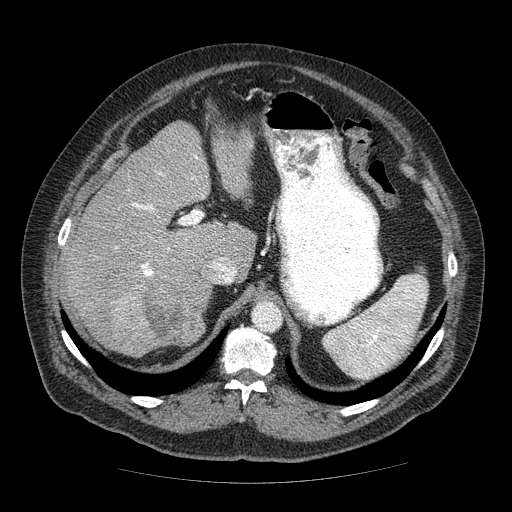
Contrast-enhanced abdominal CT (liver protocol), one axial slice; slice 41 of 85 in the series (ordered by position); soft-tissue window (W 400 / L 40 HU); 2.5 mm slice thickness; 512 × 512 image matrix, field of view 420 × 420 mm. From the clinical record (not read from this slice): diagnosis: hepatocellular carcinoma (patient treated with transarterial chemoembolisation; whether this scan precedes or follows treatment is not stated here); TNM stage (as recorded): Stage-IIIA; Child-Pugh class: A; tumour nodularity: multinodular; tumour size: 7 cm.
Outlined on this slice (semi-automatic segmentation, software-assisted and operator-edited):
- liver parenchyma outside the tumour (the mass and vessels are separate outlines, so this box may not span the whole liver): bounding box <64,120,256,356> (left, top, right, bottom; pixels)
- mass: <100,268,210,356>
- liver vessels: <115,155,198,276>